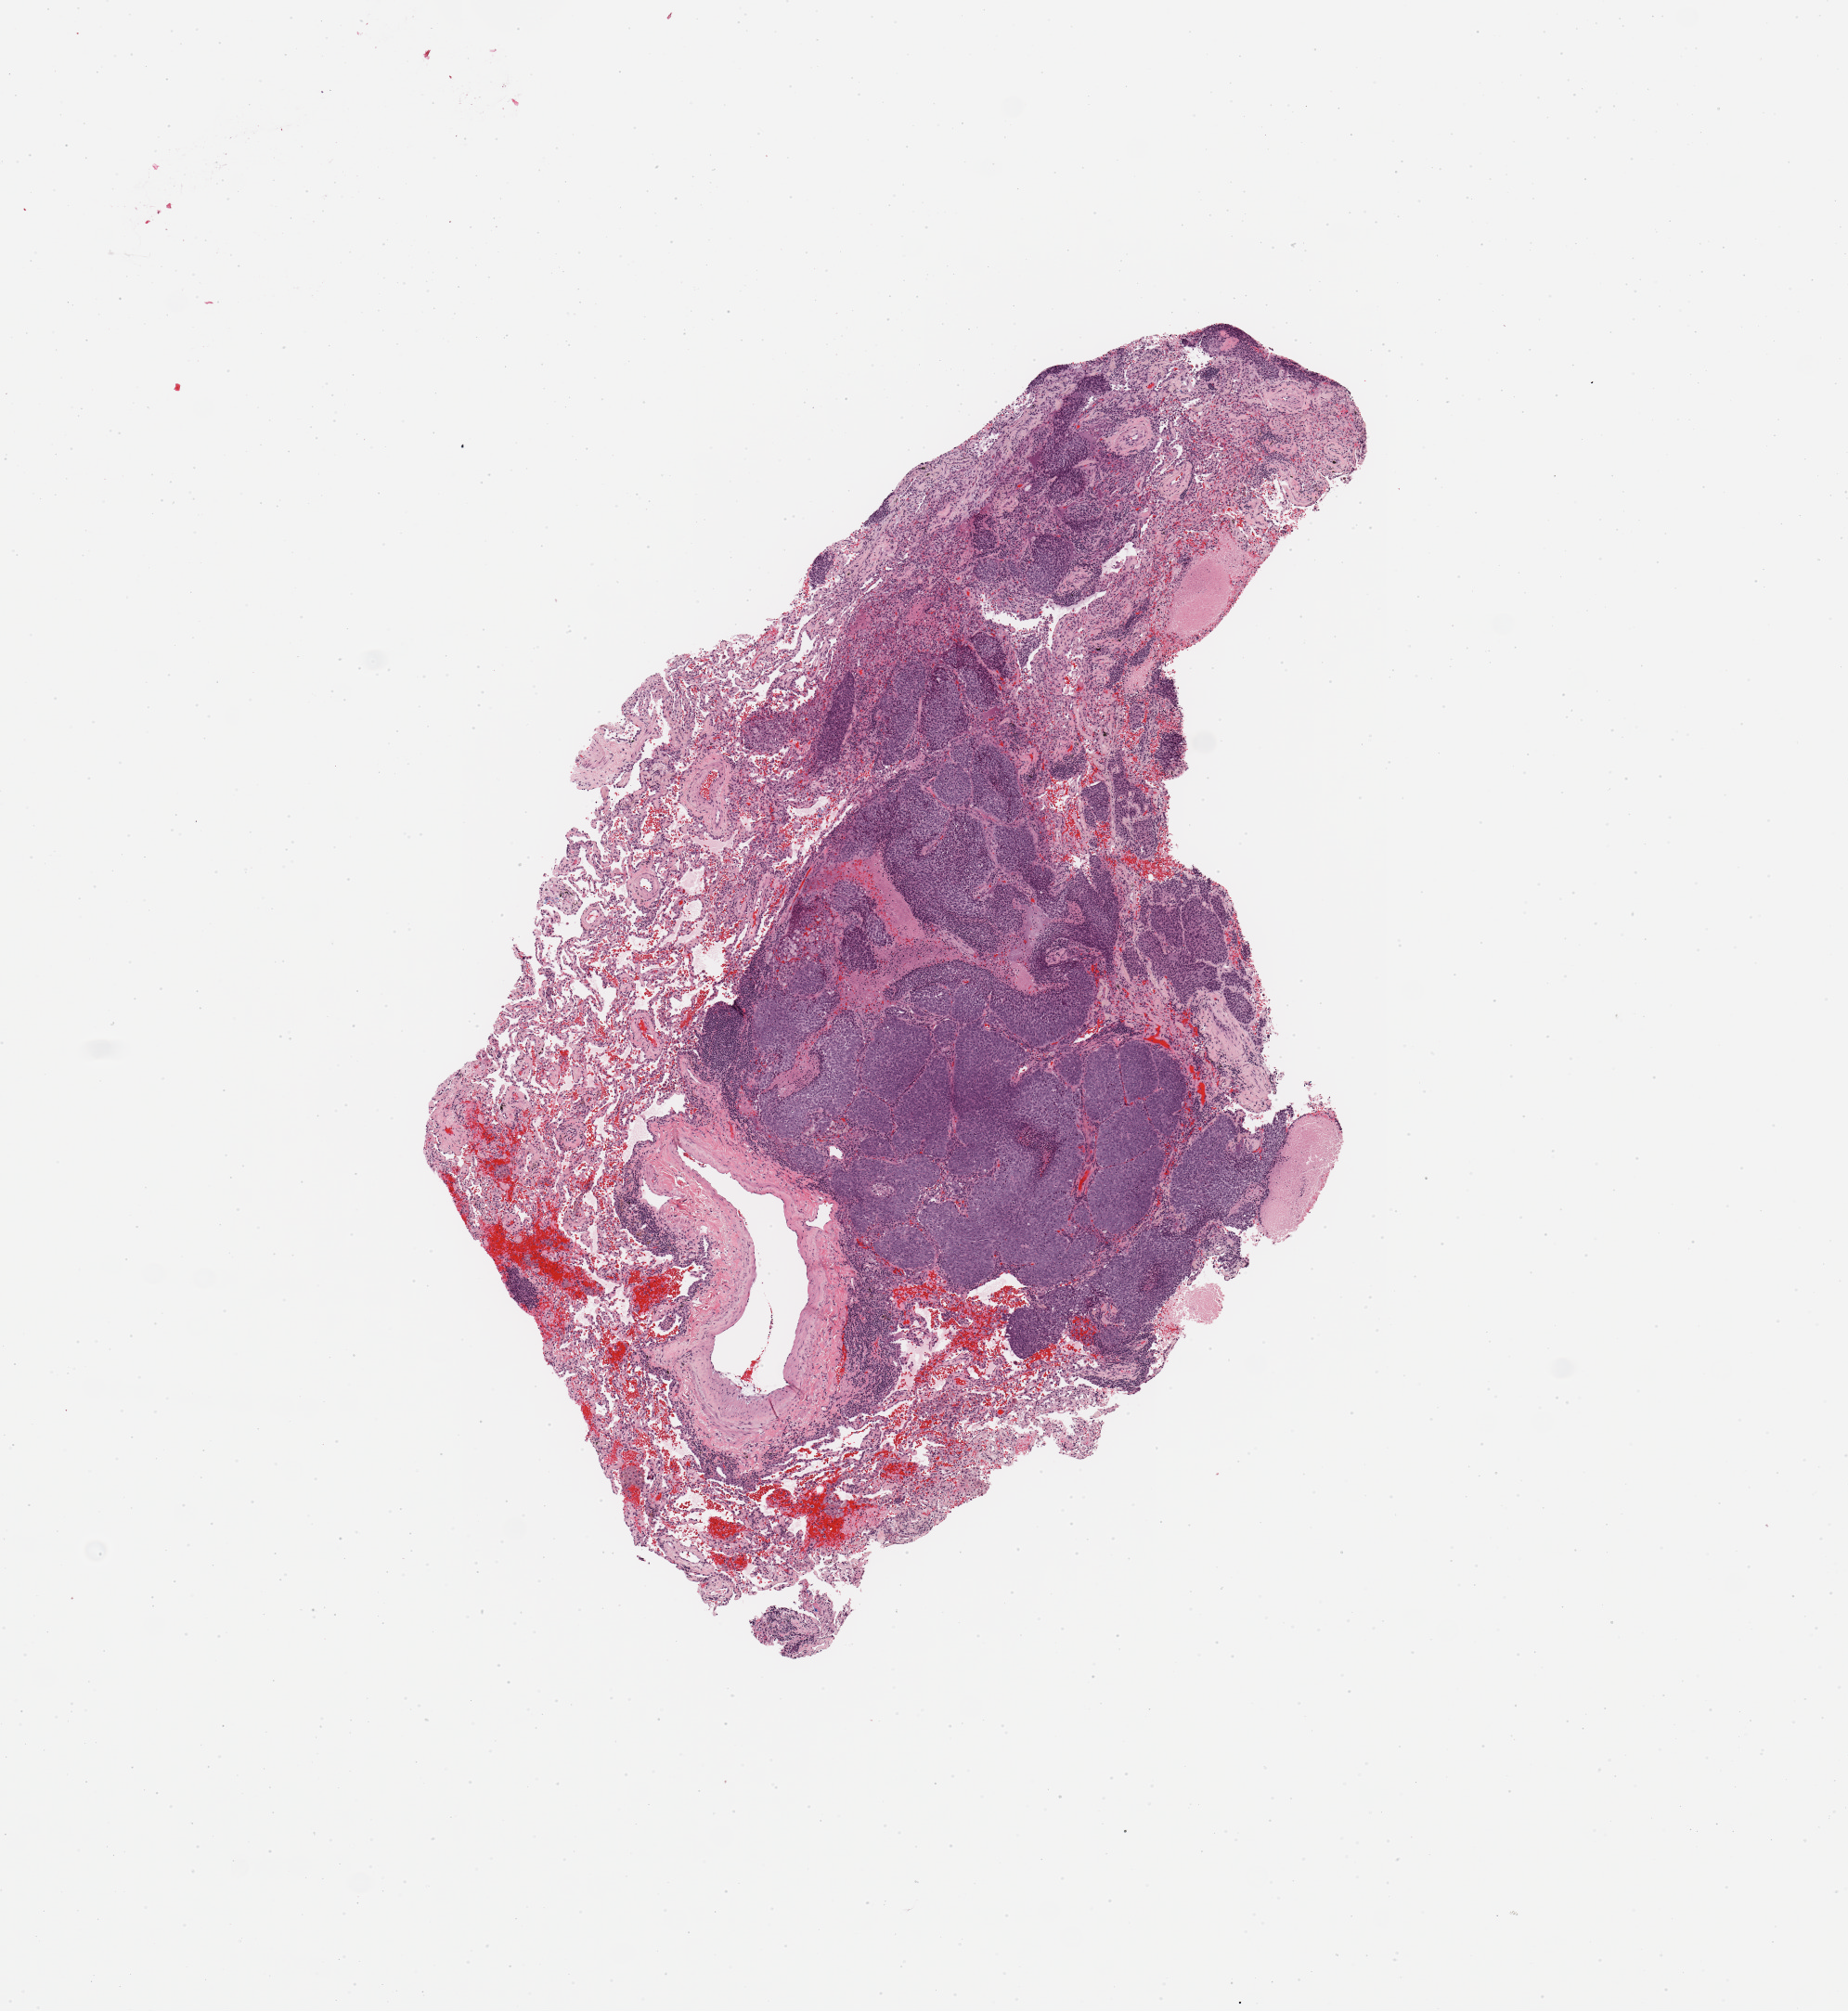
Digitized H&E tissue section (whole slide) — shown as a low-resolution overview of the whole scanned area (about 7.9 x 8.6 mm). Tumour tissue sample, lung. Male, 72 y/o. Histologic grade: G3 (poorly differentiated).
- diagnosis: Squamous cell carcinoma, NOS
- primary tumour site (as recorded): right upper lobe
- AJCC pathologic stage: IA